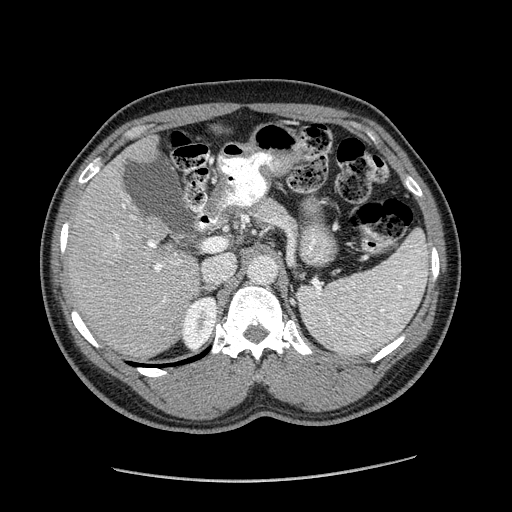
Contrast-enhanced abdominal CT (liver protocol), one axial slice; position 109 of 182 along the scan axis; reconstruction kernel STANDARD; 120 kVp; soft-tissue window (W 400 / L 40 HU); 2.5 mm slice thickness; 512 × 512 image matrix. Case-level facts recorded for this patient, not image findings: diagnosis: hepatocellular carcinoma (patient treated with transarterial chemoembolisation; whether this scan precedes or follows treatment is not stated here); TNM stage (as recorded): Stage-I; Child-Pugh class: A; tumour nodularity: uninodular.
Annotated regions visible in this slice (semi-automatic segmentation, software-assisted and operator-edited):
- liver parenchyma outside the tumour (the mass and vessels are separate outlines, so this box may not span the whole liver): bounding box (x1, y1, x2, y2) in pixels: (66, 136, 200, 358)
- mass: (94, 235, 123, 263)
- liver vessels: (115, 204, 182, 329)